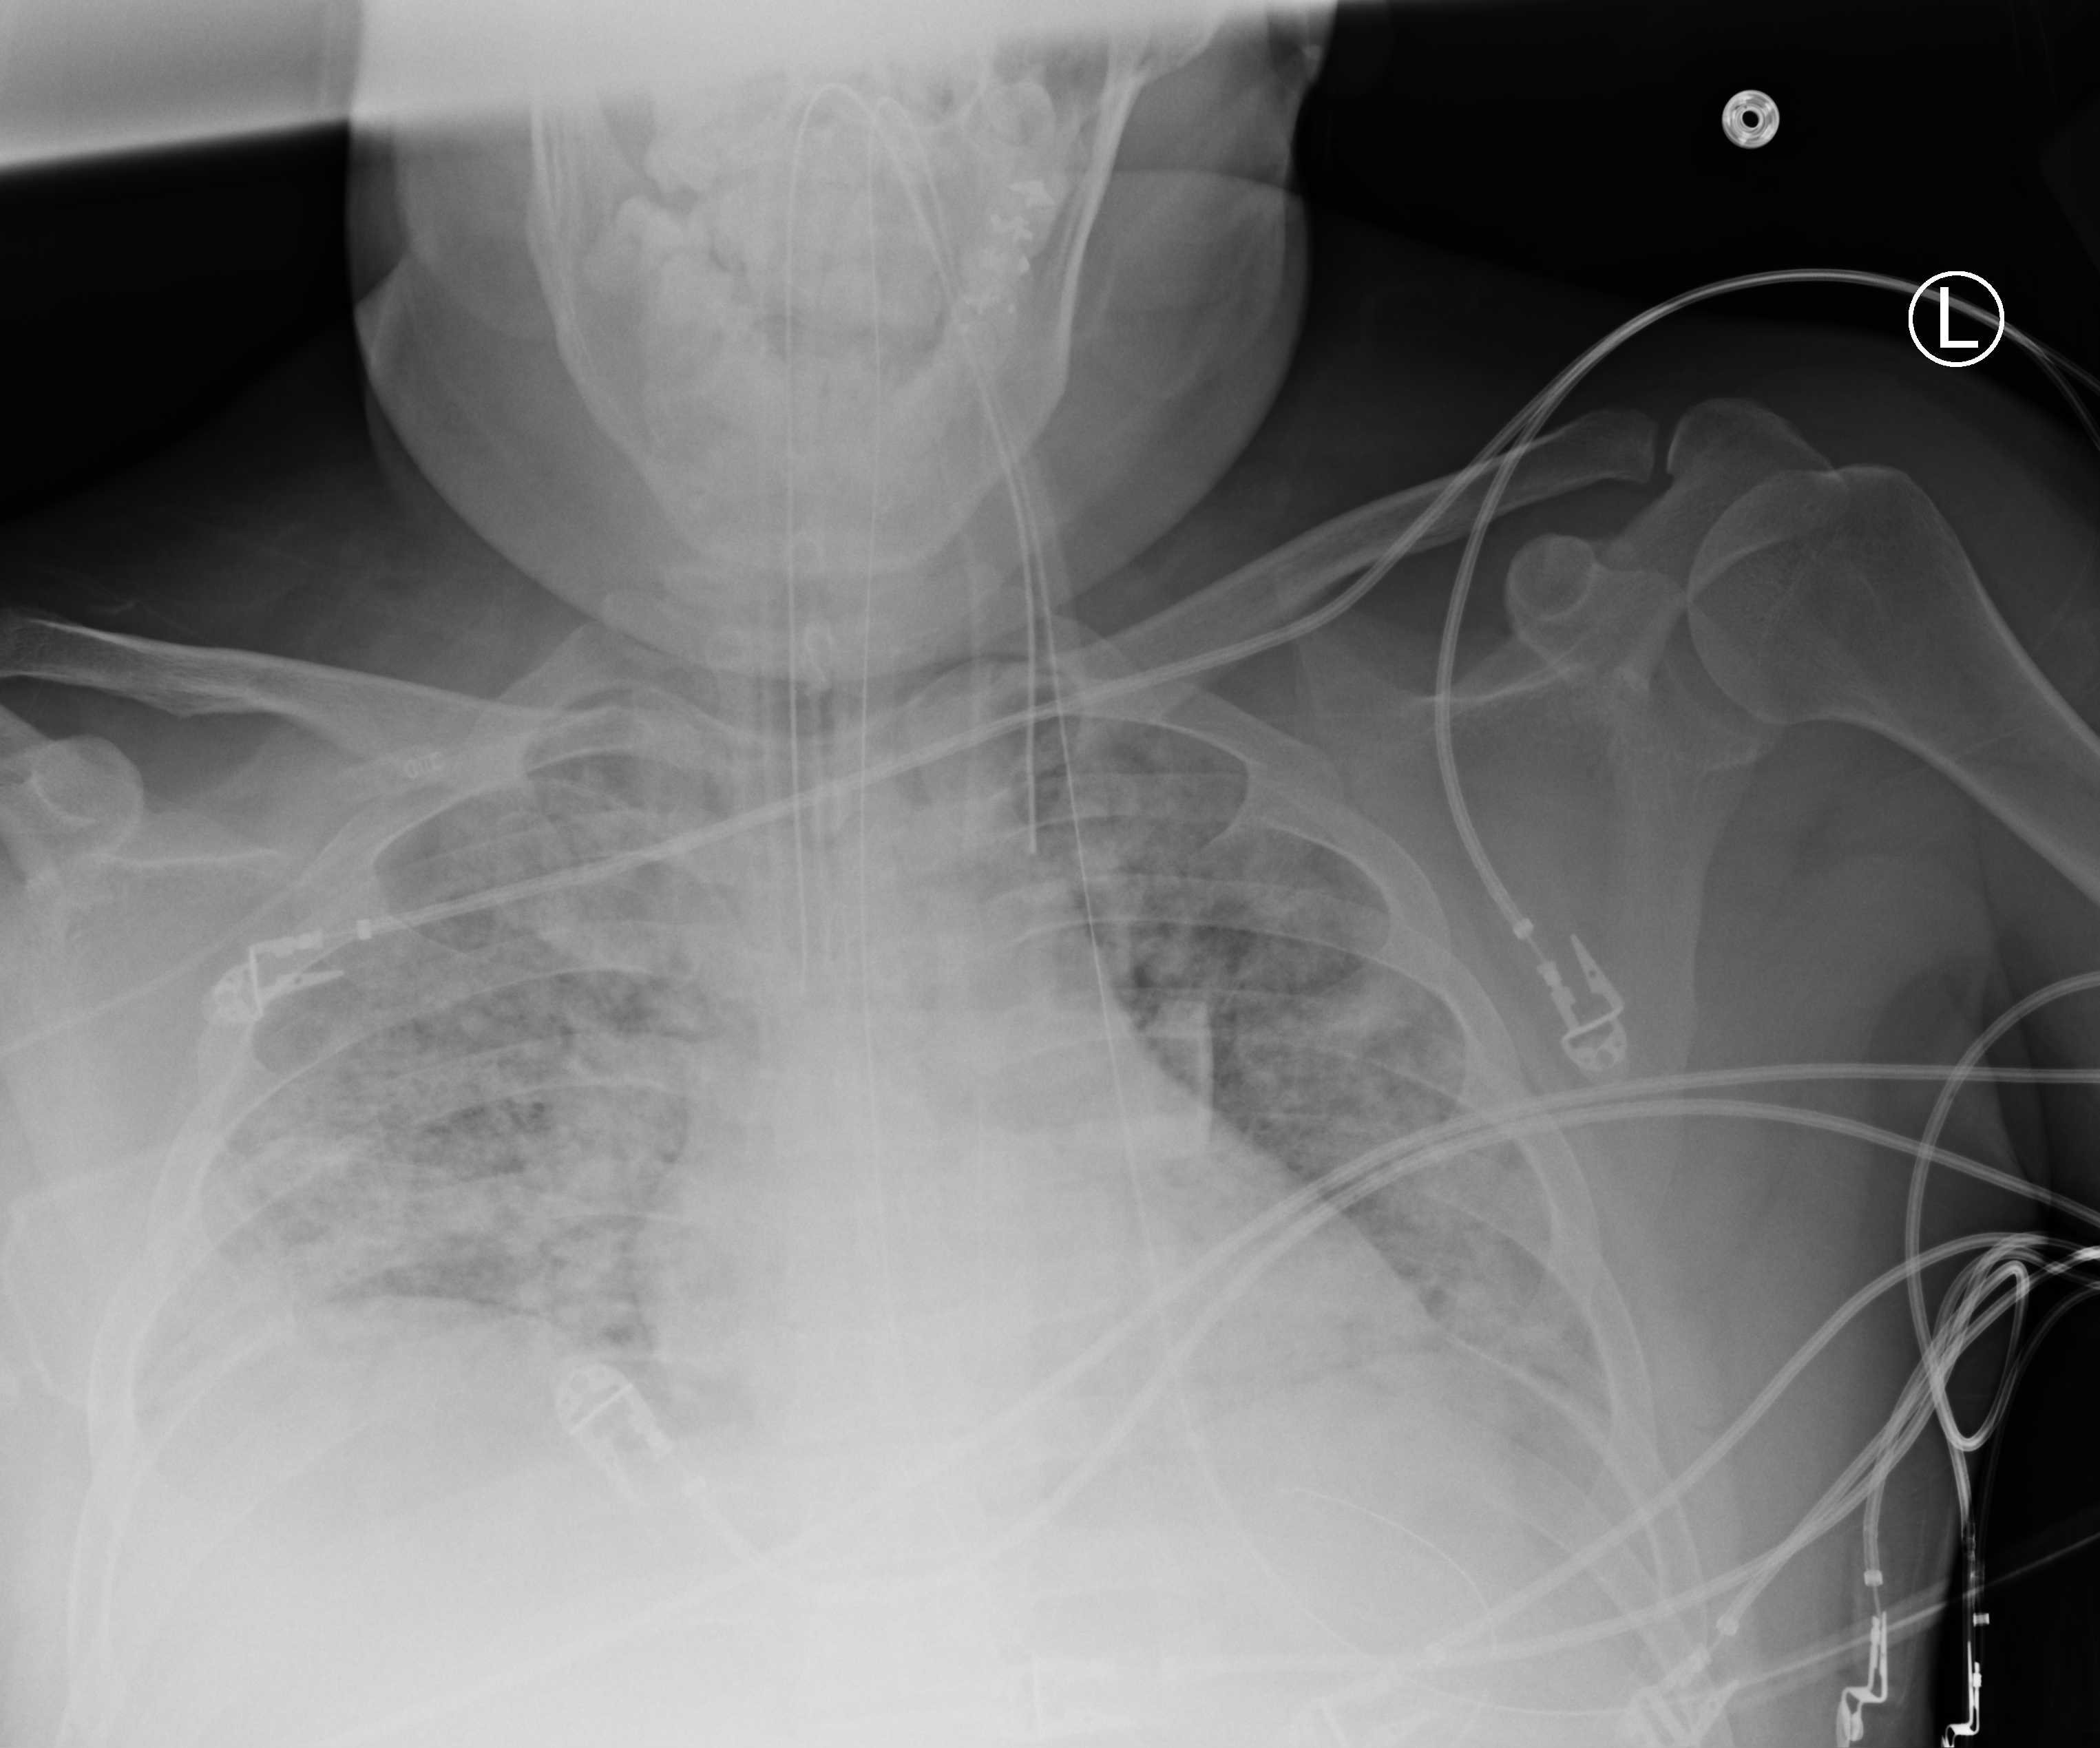
Bedside chest radiograph (computed radiography); anteroposterior (AP) projection. Patient hospitalised with COVID-19; male, aged 18–59 years.
Hospital-stay facts (about this admission, not read from this image; timing relative to this image not recorded): length of hospital stay: 44 days; admitted to intensive care during this hospital stay: yes; other chronic lung disease (admission record): no.